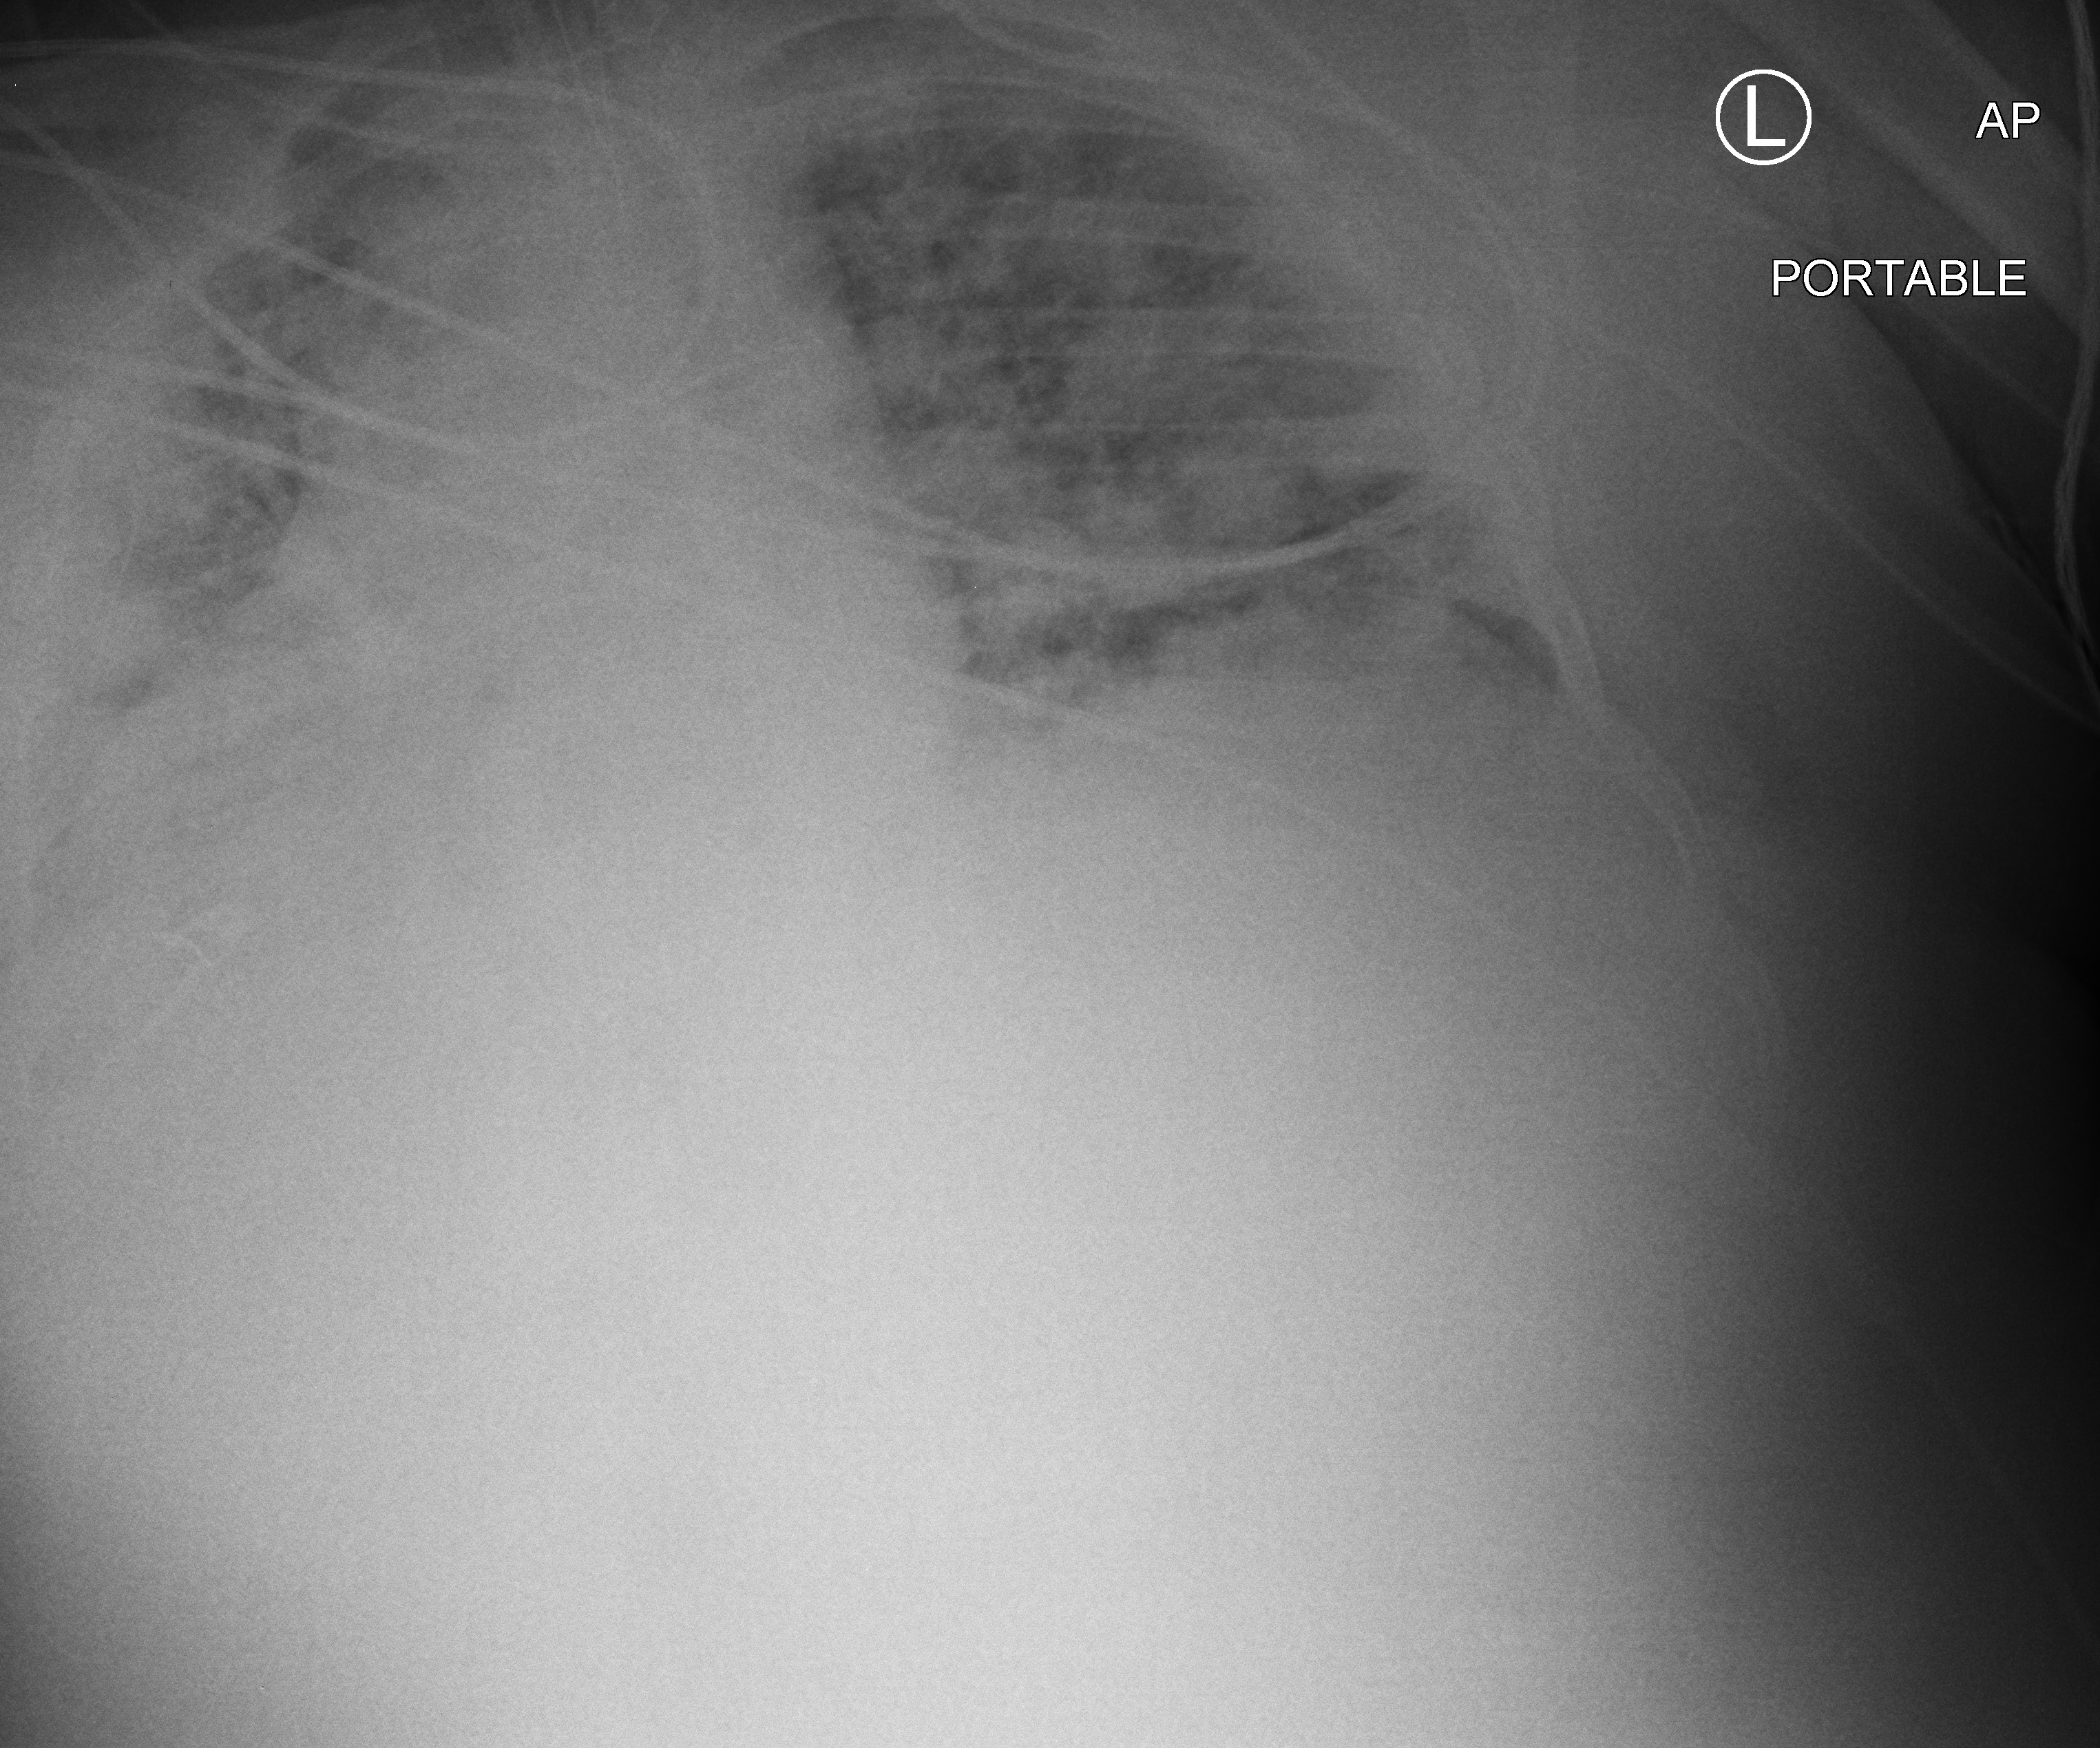
Chest X-ray (portable); anteroposterior (AP) projection. Male patient hospitalised with COVID-19, age 18–59 years.
Hospital-stay facts (about this admission, not read from this image; timing relative to this image not recorded):
- admitted to intensive care during this hospital stay: yes